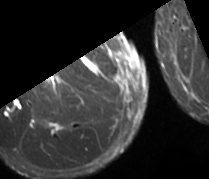
MRI of an extremity soft-tissue mass, one axial slice; position 18 of 89 along the scan axis; STIR; MR volume resampled by the dataset authors to the PET/CT grid (not the native acquisition matrix); 209 × 179 image matrix, field of view 204 × 175 mm. Male patient. Case-level facts recorded for this patient, not image findings: histological type: undifferentiated - pleiomorphic; grade: high; site of the primary tumour: right thigh.
Annotated regions visible in this slice (expert contour drawn on MRI and transferred to this co-registered scan by the dataset authors):
- gross tumour volume including surrounding oedema: bounding box (x1, y1, x2, y2) in pixels: (53, 75, 58, 81)